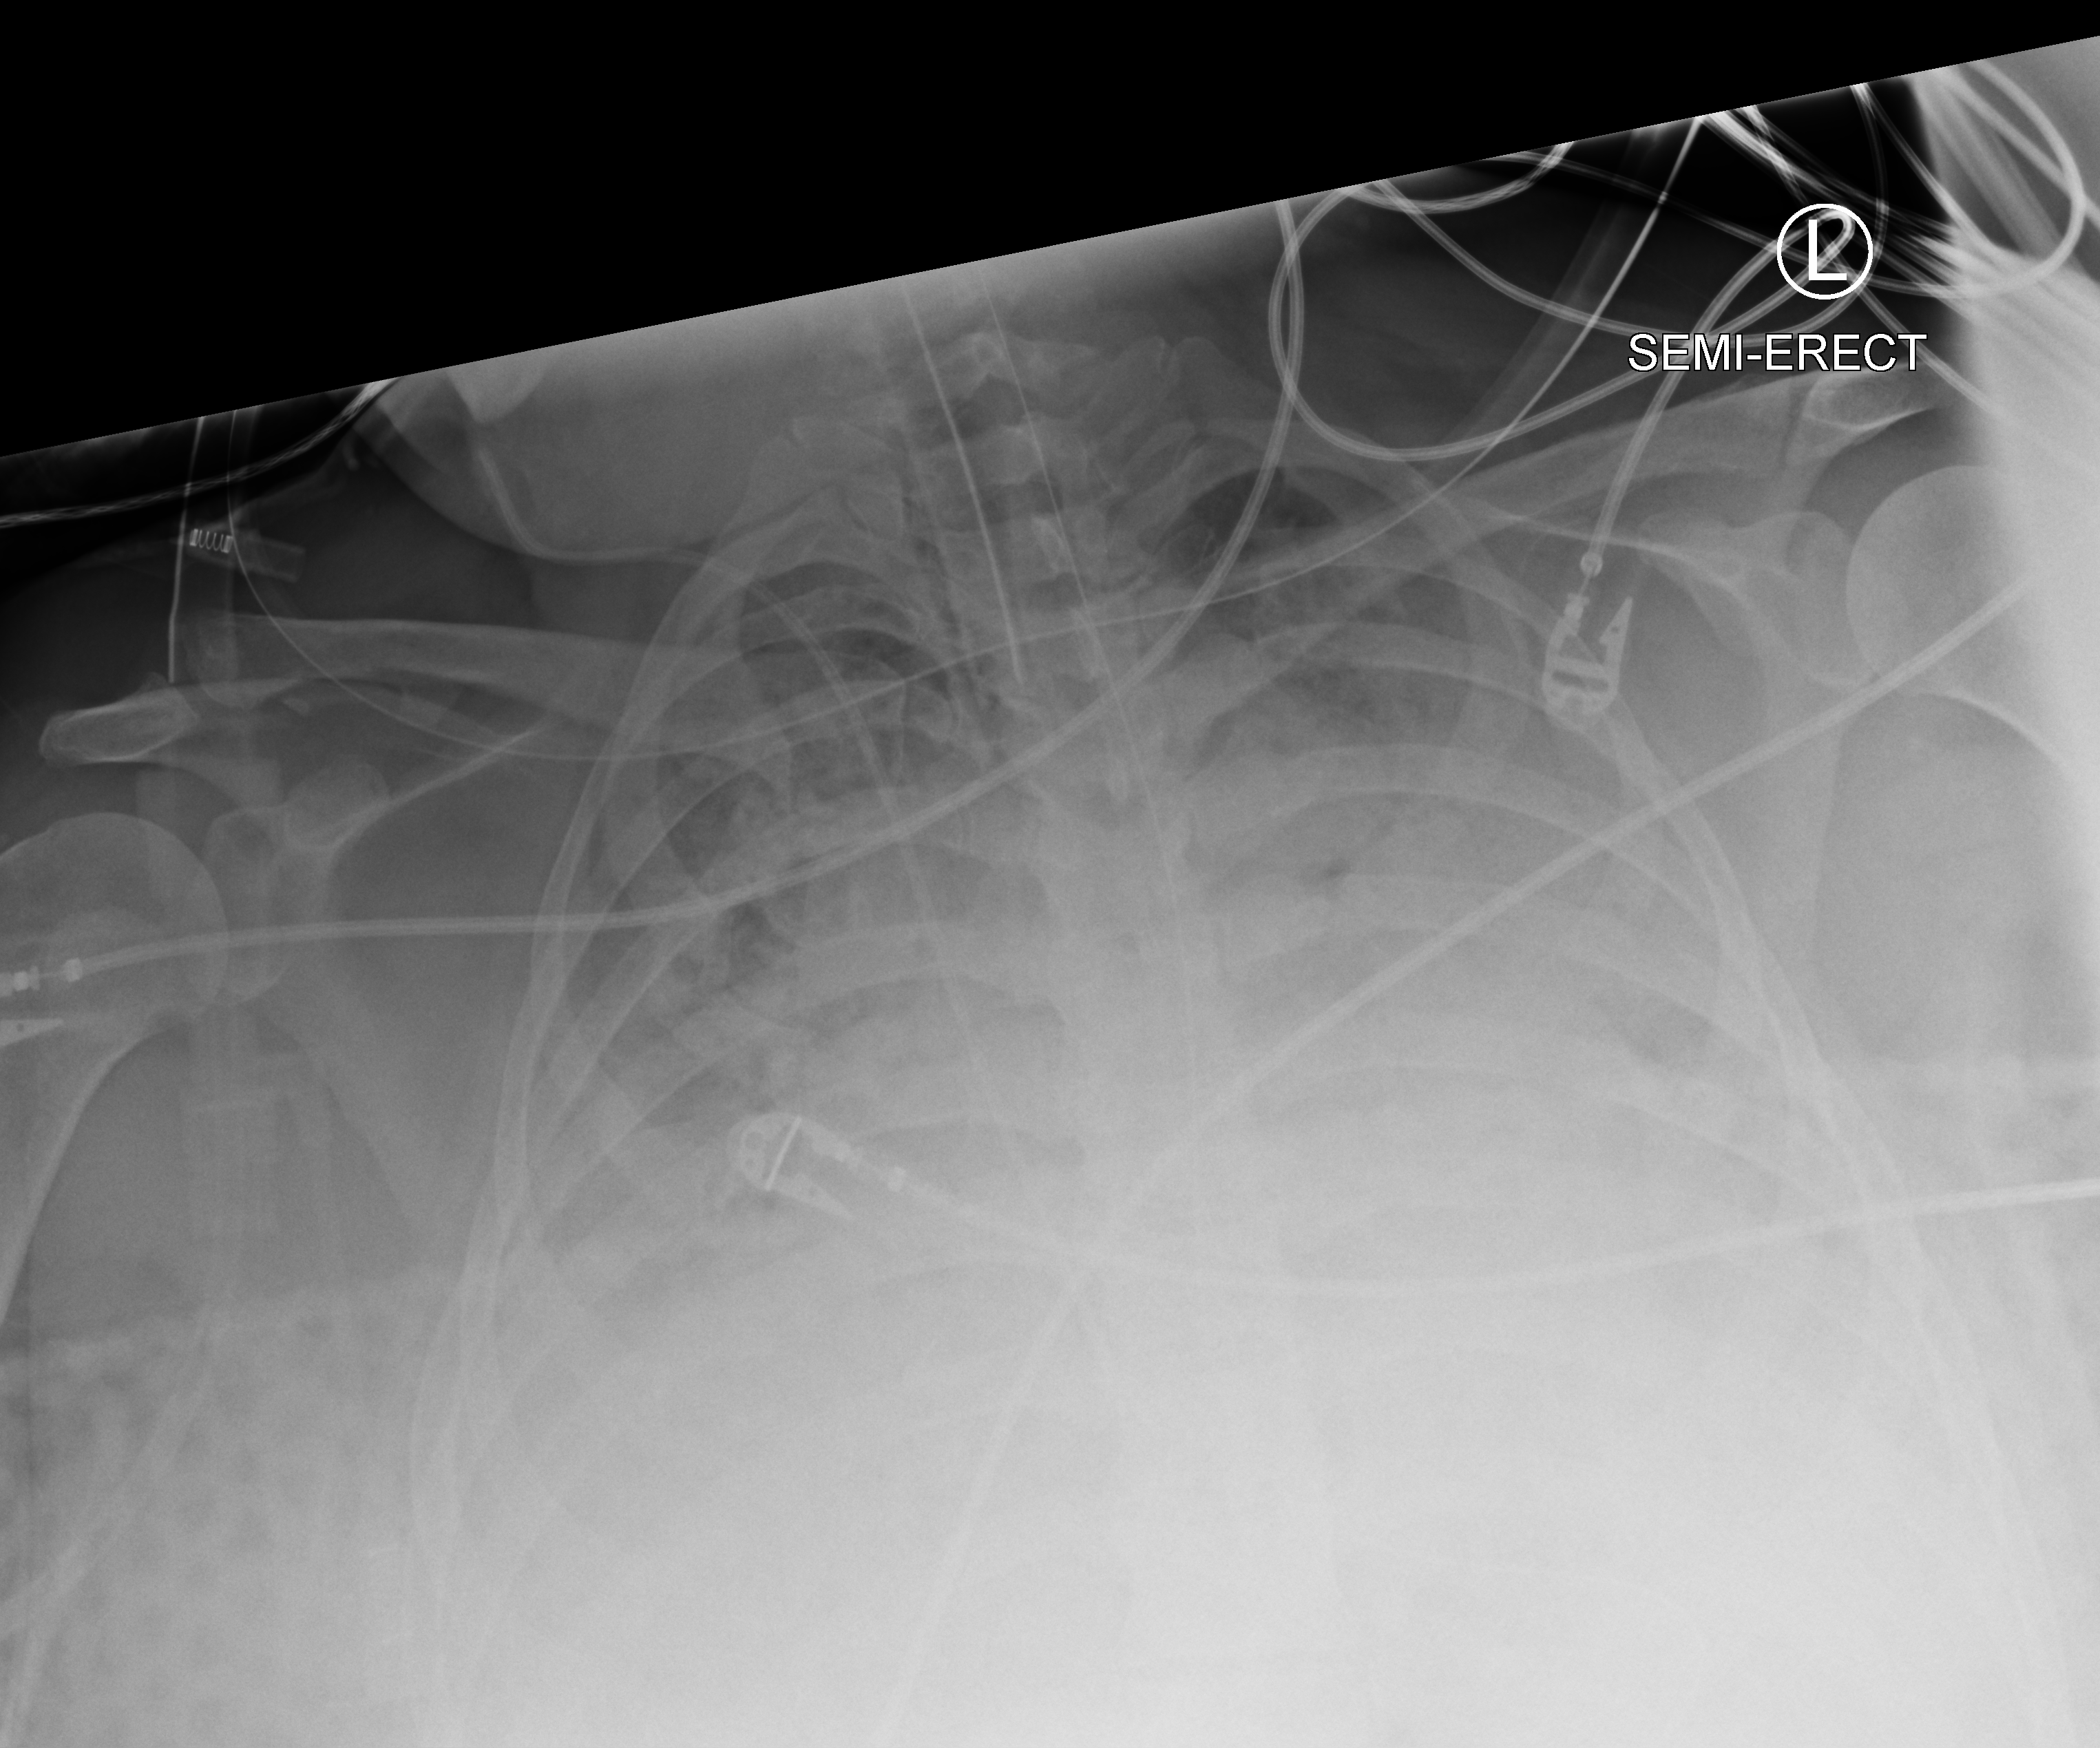
Portable chest radiograph. Female patient hospitalised with COVID-19, age 18–59 years.
Admission-level facts for this patient (not findings on this image; timing relative to this image not recorded): admitted to intensive care during this hospital stay: yes; chronic kidney disease (admission record): no.